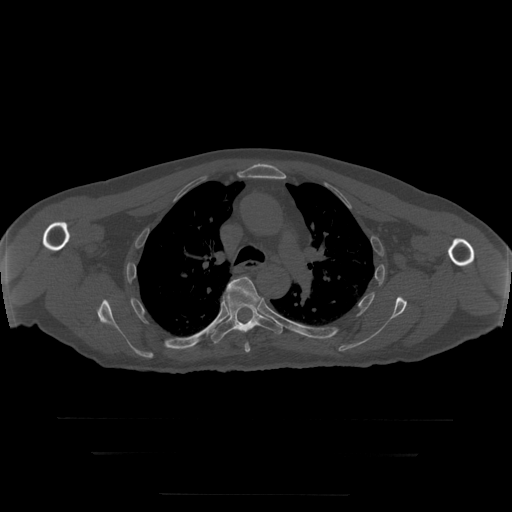
CT including the spine, one axial slice. Slice 214 of 397 in the series (ordered by position). Reconstruction kernel STANDARD. 120 kVp. Bone window (W 1800 / L 400 HU). 1.25 mm slice thickness. 512 × 512 image matrix, field of view 510 × 510 mm. Patient age 73 years. From the clinical record (not read from this slice): primary cancer: prostate.
Structures marked on this image (semi-automatically segmented with operator editing):
- T5 vertebra: bounding box (x1, y1, x2, y2) in pixels: (227, 277, 260, 353)
- T6 vertebra: (211, 295, 283, 344)